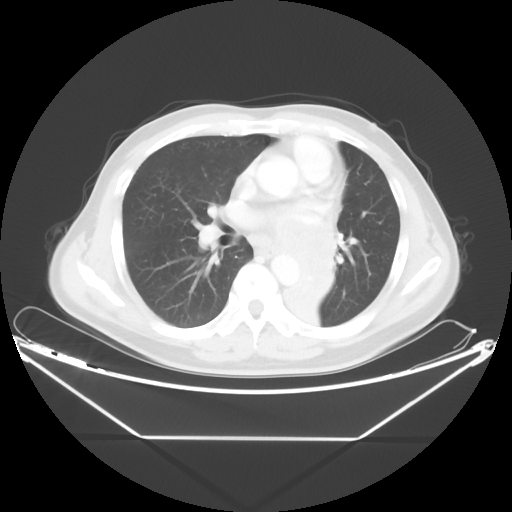
Chest CT, one axial slice. Position 24 of 48 along the scan axis. Reconstruction kernel STANDARD. 120 kVp. Lung window (W 1500 / L -600 HU). 5 mm slice thickness. 512 × 512 image matrix, field of view 438 × 438 mm. Patient: male, 58 years. From the clinical record (not read from this slice): clinical TNM (as recorded): T3 N3 M0.
Outlined on this slice (rectangle marked by the reading radiologist):
- lung tumour (recorded histology: squamous cell carcinoma): bounding box (x1, y1, x2, y2) in pixels: (272, 212, 334, 325)